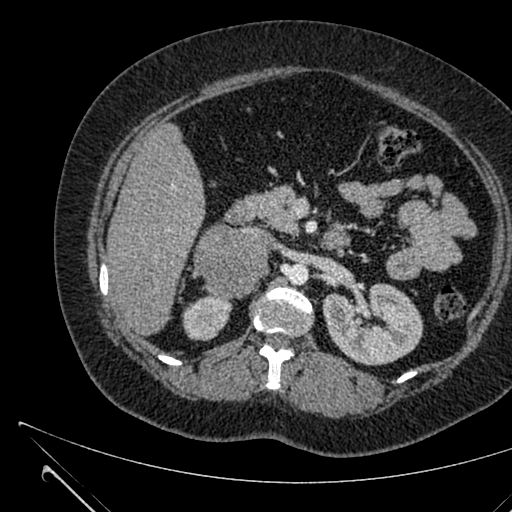
Contrast-enhanced abdominal CT, one axial slice. Intravenous contrast given. Soft-tissue window (W 400 / L 40 HU). 1 mm slice thickness. 512 × 512 image matrix, field of view 376 × 376 mm. Female patient, age 36 years. From the clinical record (not read from this slice): diagnosis: adrenocortical carcinoma; tumour side: right adrenal; tumour size at pathology: 10 cm; Ki-67 index: 20 %; stage (as recorded): 4.
Structures marked on this image (semi-automatic segmentation, software-assisted and operator-edited):
- mass: bounding box <194,226,269,301> (left, top, right, bottom; pixels)